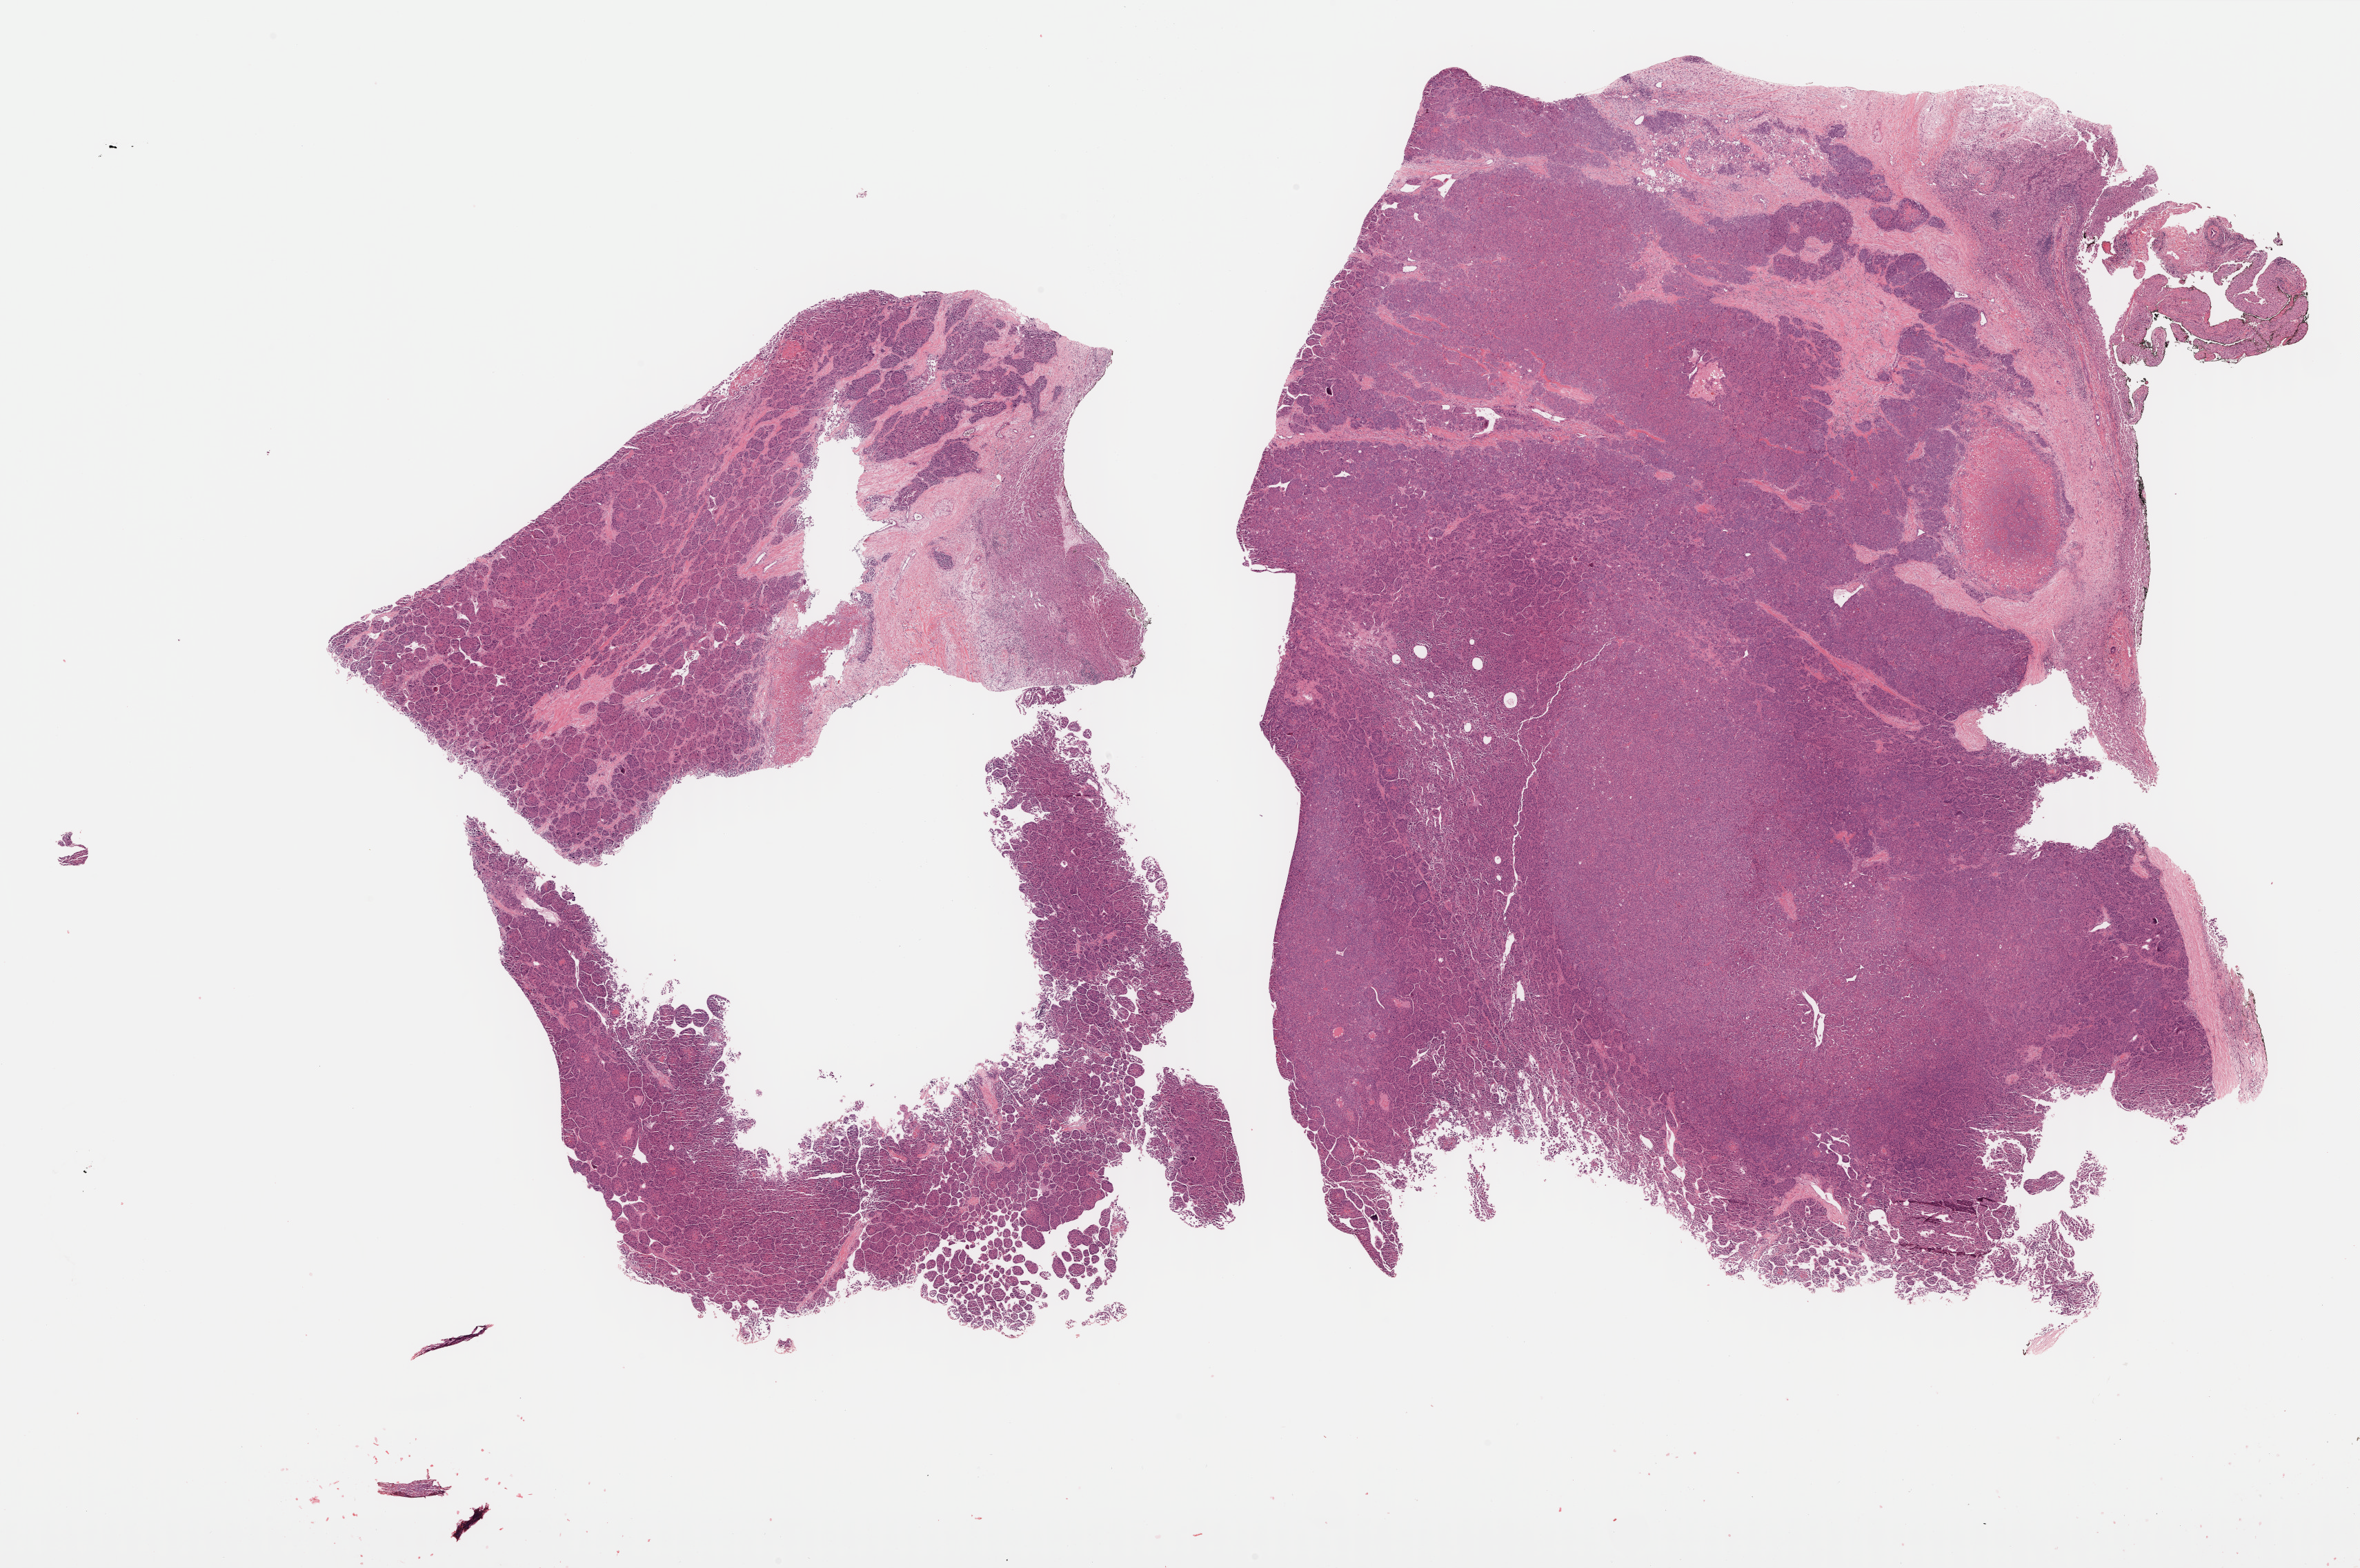
Hematoxylin and eosin (H&E) stained whole-slide image — a low-resolution overview of the entire scanned area, about 27.7 x 18.4 mm (slide scanned at 40x). FFPE section. Liver, primary tumour sample. Female, age 73 years at initial diagnosis. Histologic grade: G3 (poorly differentiated).
AJCC pathologic stage: I (6th edition). Histologic diagnosis: Hepatocellular carcinoma, NOS. TNM: T1 N0 M0.